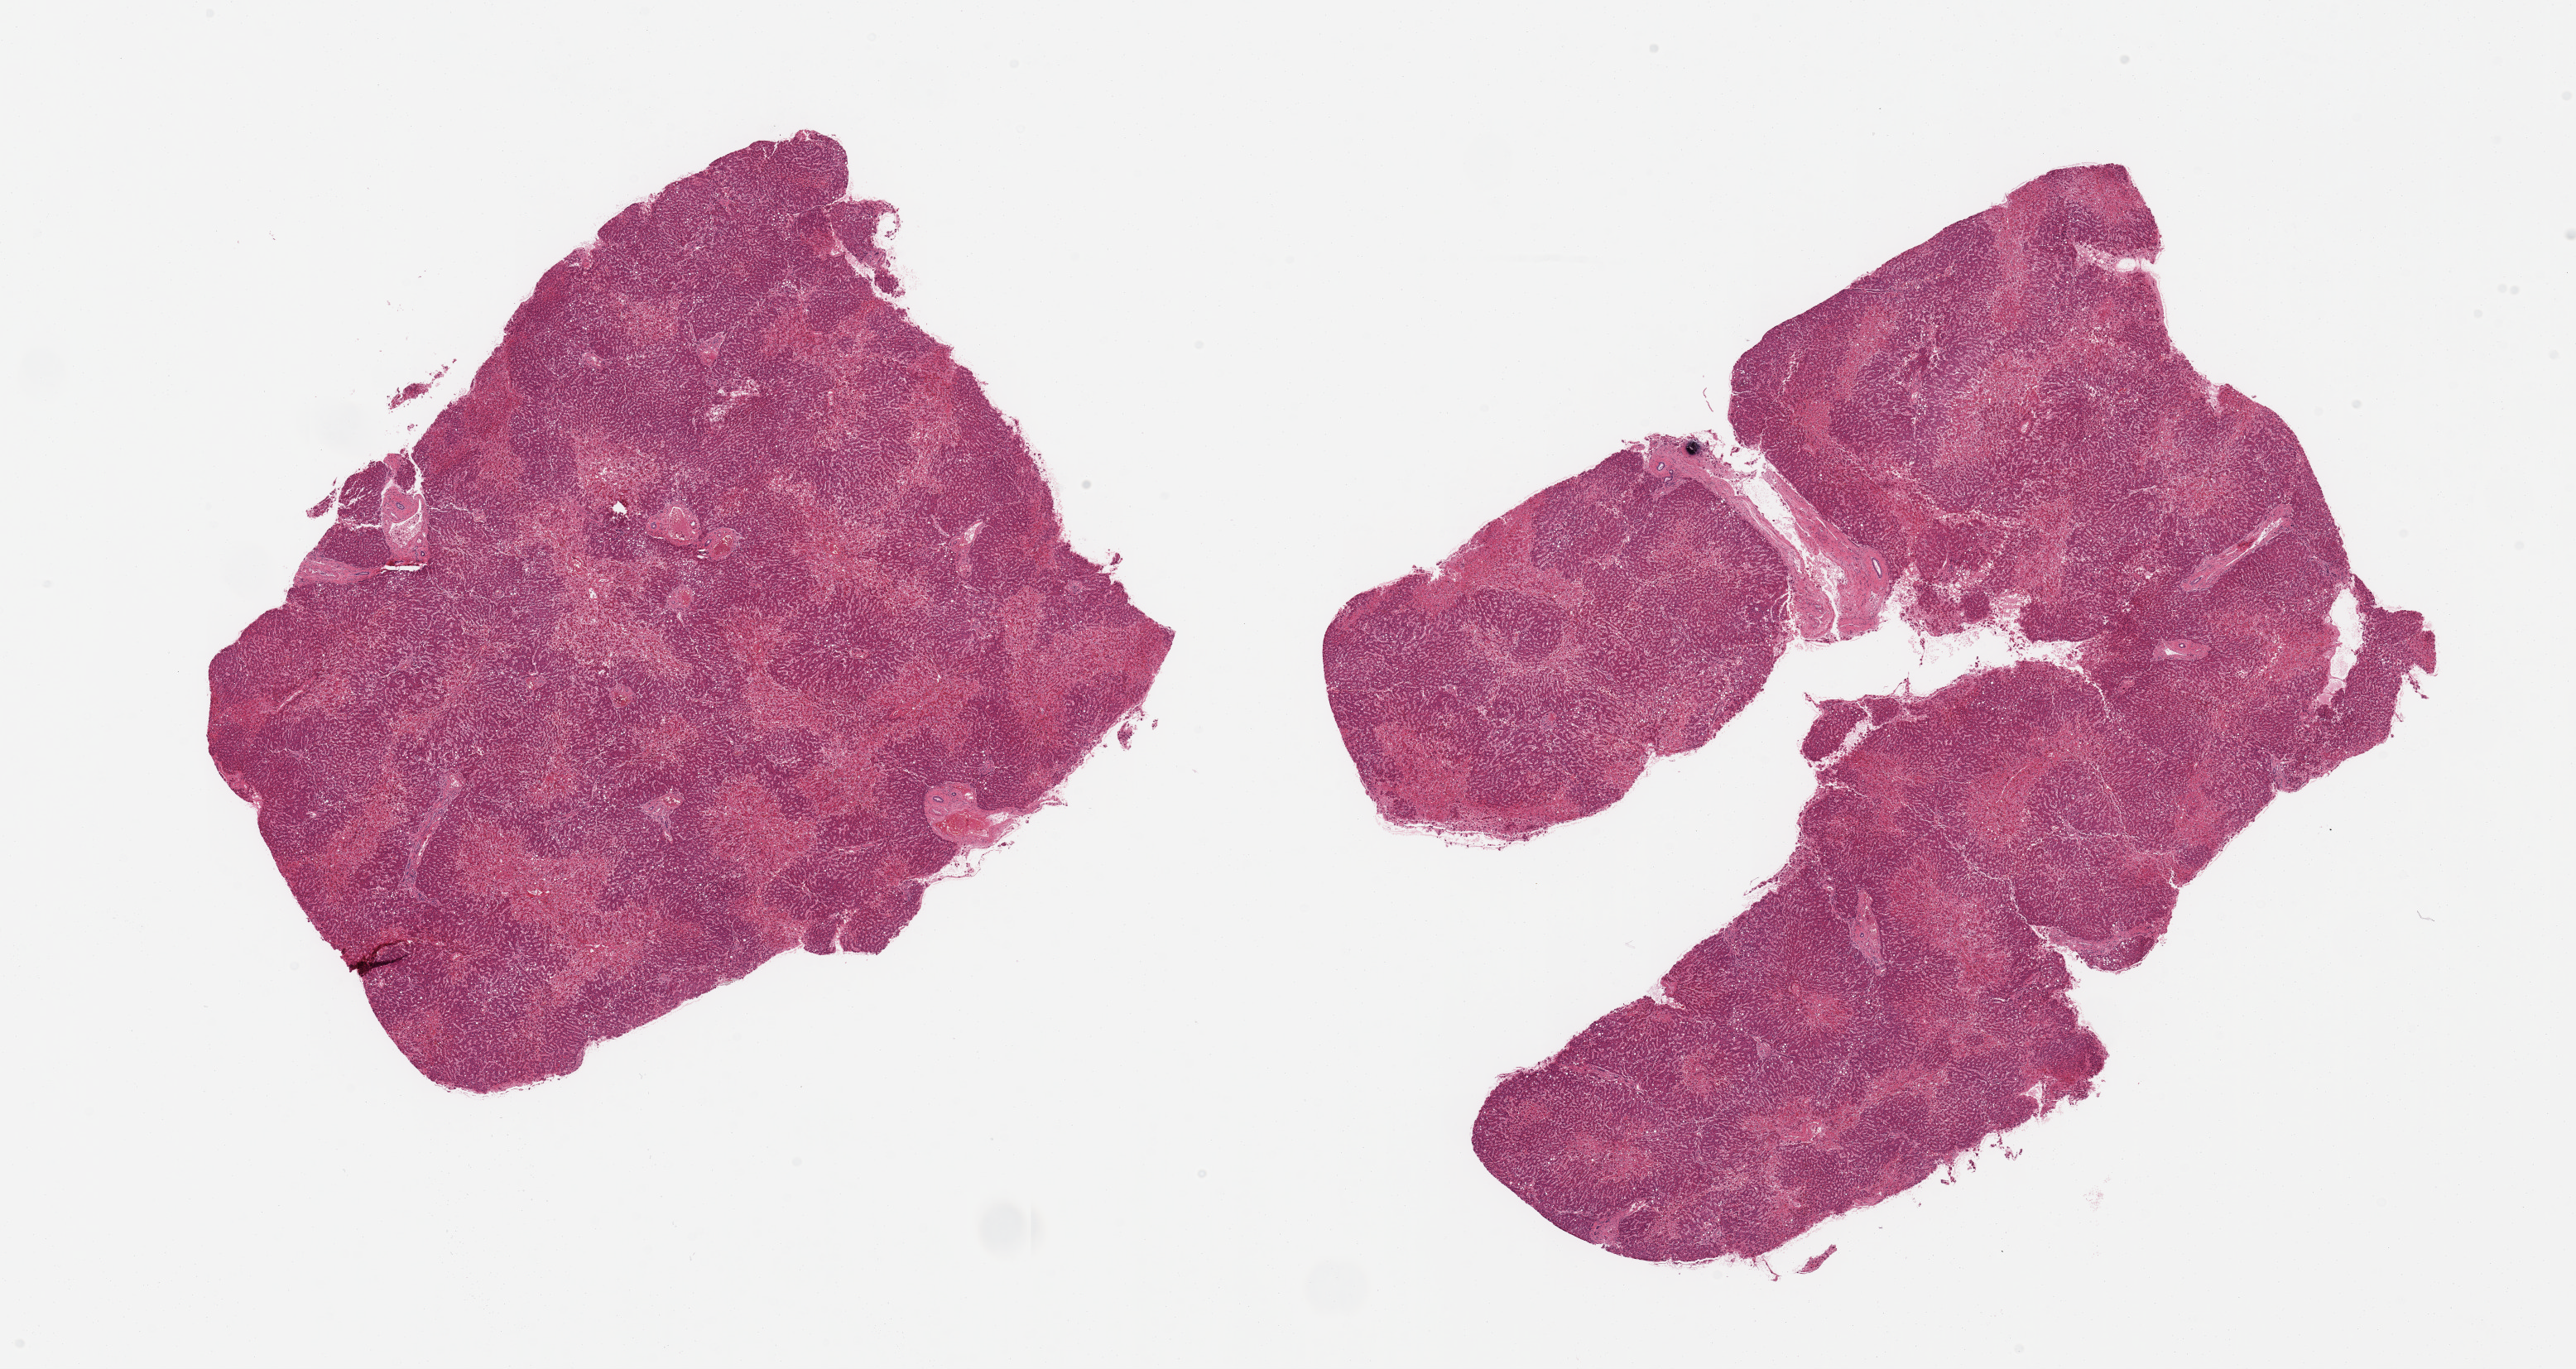
Digitized H&E-stained section, shown as a low-resolution overview of the whole scanned area (about 24.6 x 13.1 mm, slide scanned at 20x), PAXgene-fixed, paraffin-embedded tissue, sampled site (target tissue): liver, donor tissue sample. Female donor.
- reviewer comment on this tissue sample: 2 pieces, marked cardiac congestion